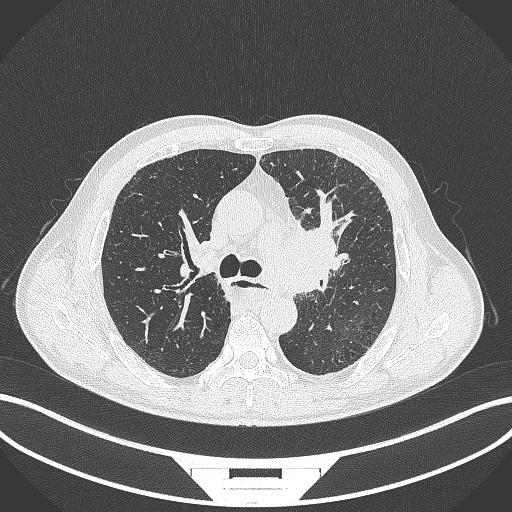
Chest CT, one axial slice. Slice 249 of 411 in the series (ordered by position). Lung window (W 1500 / L -600 HU). 1 mm slice thickness. 512 × 512 image matrix. Male patient, age 57 years. Case-level facts recorded for this patient, not image findings: clinical TNM (as recorded): T2a N1 M0.
Annotated regions visible in this slice (rectangle marked by the reading radiologist):
- lung tumour (recorded histology: squamous cell carcinoma): bounding box <270,209,348,303> (left, top, right, bottom; pixels)